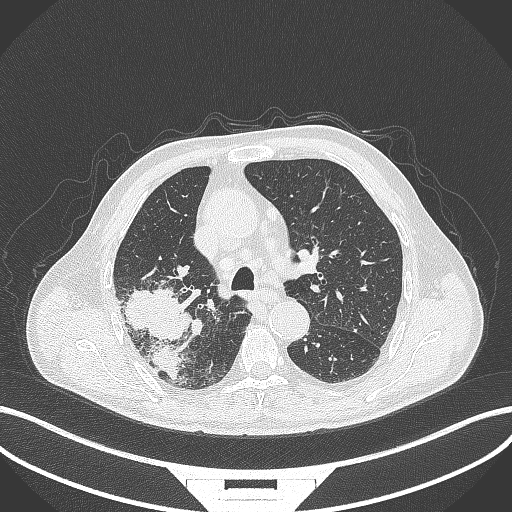
Chest CT, one axial slice. Position 279 of 429 along the scan axis. Lung window (W 1500 / L -600 HU). 1 mm slice thickness. 512 × 512 image matrix, field of view 400 × 400 mm. Patient: male, 72 years. Case-level facts recorded for this patient, not image findings: clinical TNM (as recorded): T3 N2 M0.
Structures marked on this image (bounding box drawn by a radiologist):
- lung tumour (recorded histology: adenocarcinoma): bounding box (x1, y1, x2, y2) in pixels: (121, 285, 199, 383)